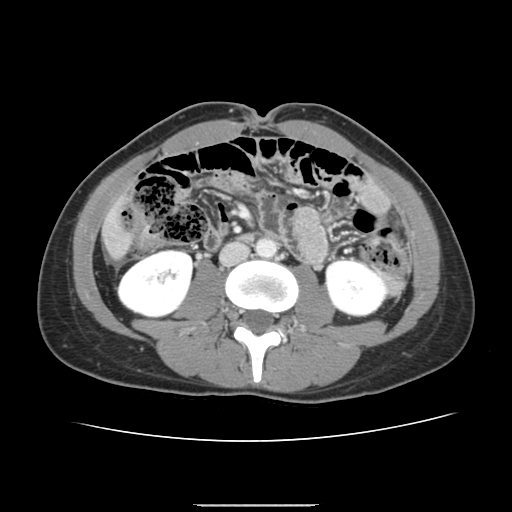
Contrast-enhanced abdominal CT, one axial slice; position 36 of 150 along the scan axis; soft-tissue window (W 400 / L 40 HU); 2.5 mm slice thickness; 512 × 512 image matrix, field of view 324 × 324 mm. Female patient, age 32 years. From the clinical record (not read from this slice): diagnosis: colorectal cancer liver metastases, imaged before liver resection; multiple liver metastases: yes; largest metastasis: 0.7 cm; disease in both lobes: no.
Annotated regions visible in this slice (outlined manually by an expert reader):
- liver: box from (x=106, y=222) to (x=128, y=256) px
- planned liver remnant (the part of the liver to remain after resection): (x=106, y=218)–(x=128, y=256)